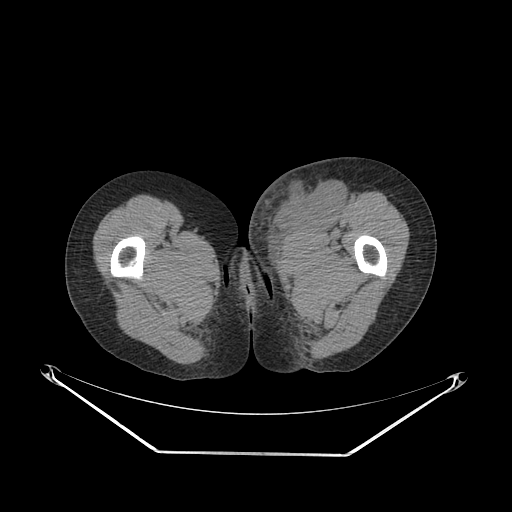
CT of an extremity soft-tissue mass (from a PET/CT study), one axial slice. Position 48 of 267 along the scan axis. Reconstruction kernel SOFT. Soft-tissue window (W 400 / L 40 HU). 512 × 512 image matrix, field of view 500 × 500 mm. Female patient. From the clinical record (not read from this slice): histological type: leiomyosarcoma; grade: high; site of the primary tumour: groin.
Outlined on this slice (expert contour drawn on MRI and transferred to this co-registered scan by the dataset authors):
- gross tumour volume including surrounding oedema: bounding box <247,171,346,245> (left, top, right, bottom; pixels)
- gross tumour volume (mass): <272,183,344,229>